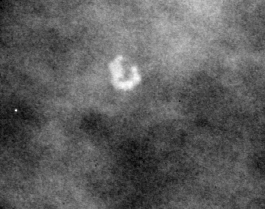
Cropped region of a digitized screen-film mammogram centred on a radiologist-marked abnormality; left breast; MLO view.
- Marked abnormality: calcifications, morphology round and regular / lucent center; BI-RADS assessment category 2; benign without callback (not worked up further).